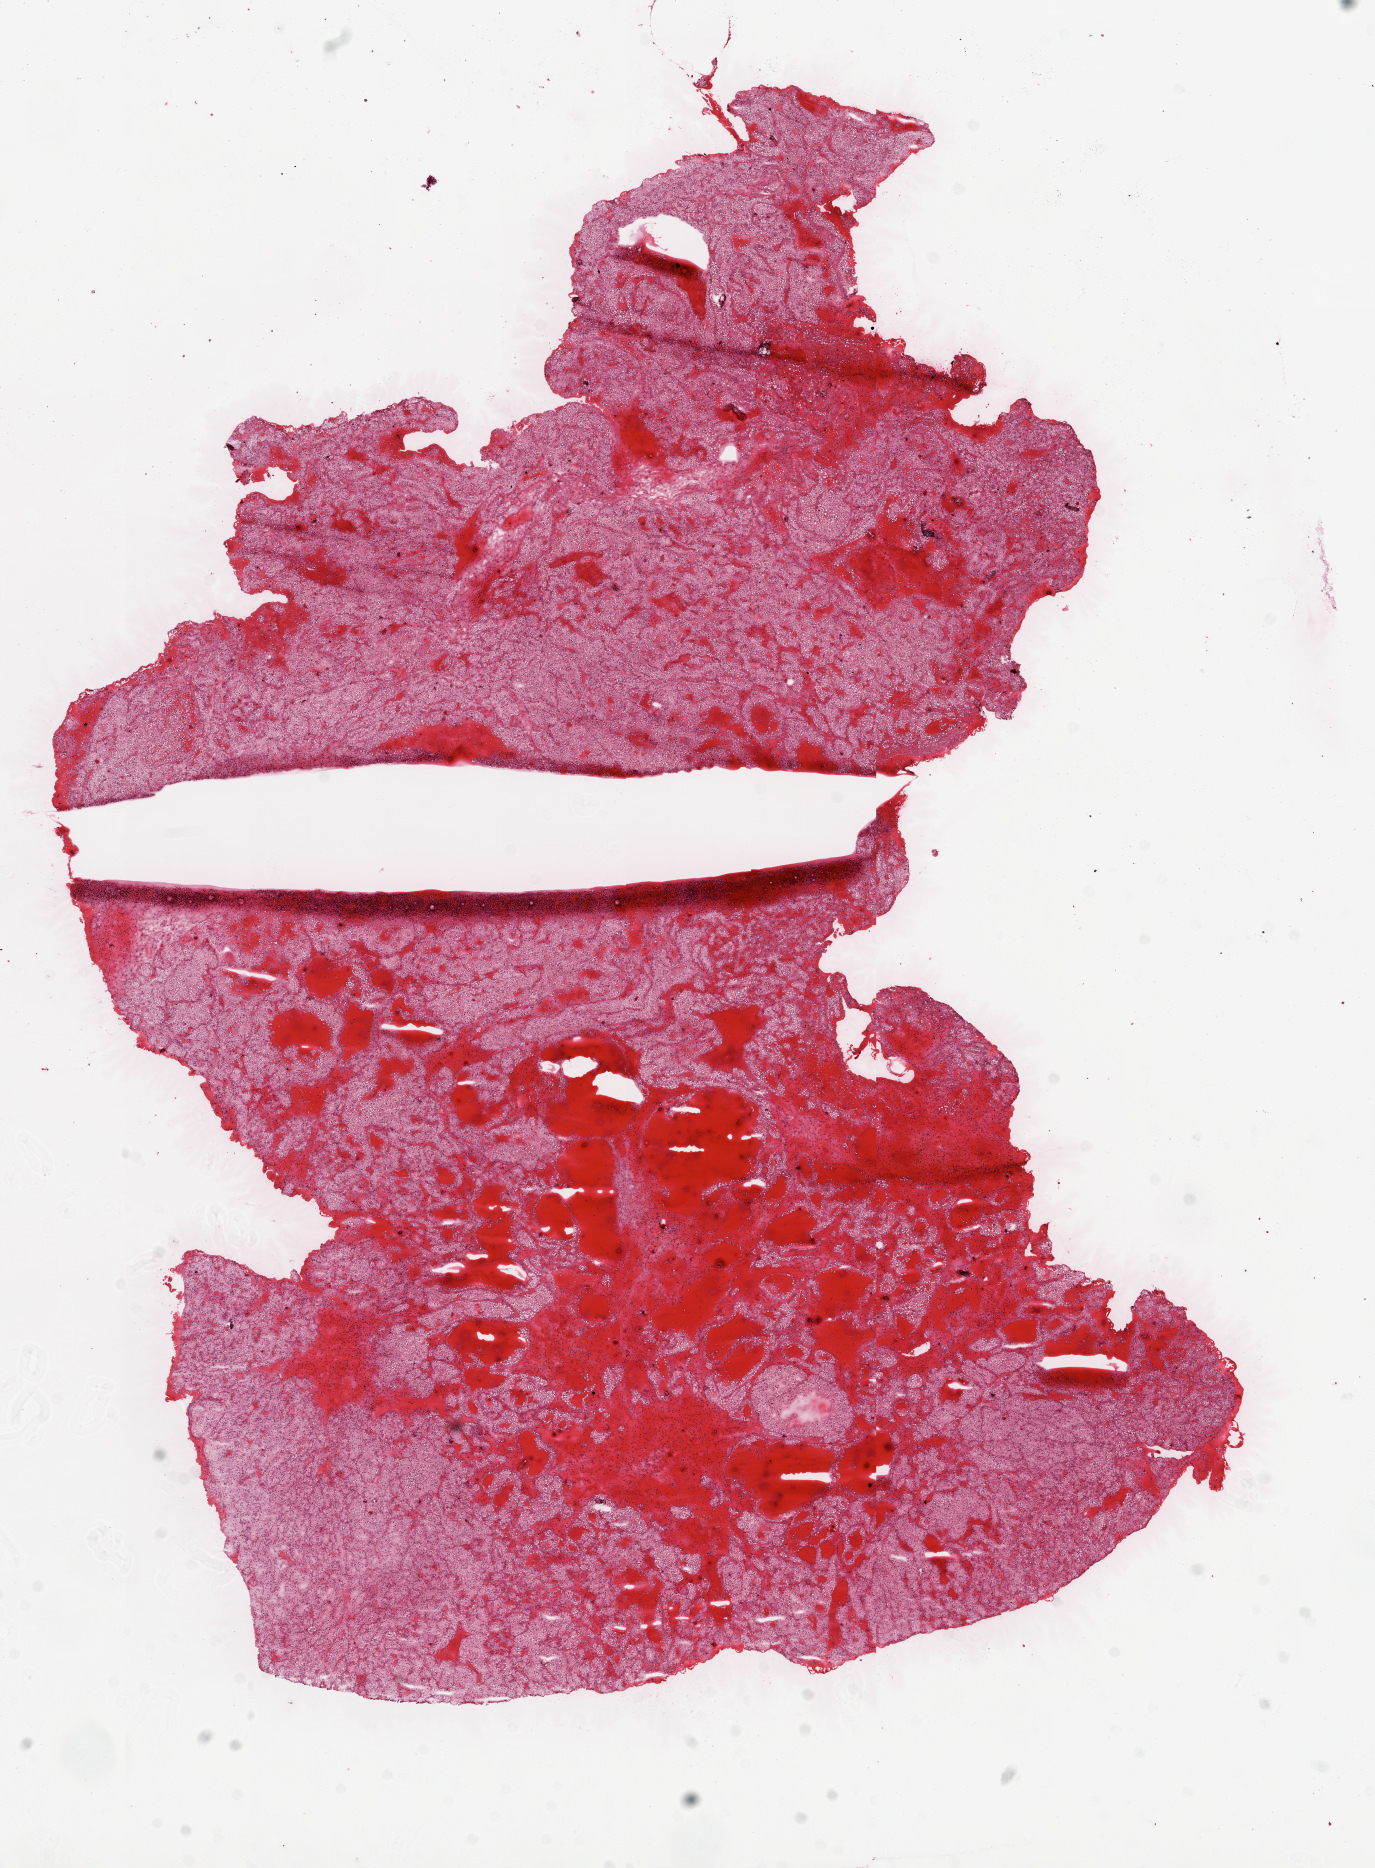
Digitized Hematoxylin and eosin (H&E) stained tissue section (whole slide), low-resolution overview of the scanned area, about 11.0 x 15.0 mm, frozen section from the top of the tissue portion, kidney, primary tumour sample. Male, age 53 years at initial diagnosis.
Pathologic diagnosis: Clear cell adenocarcinoma, NOS.